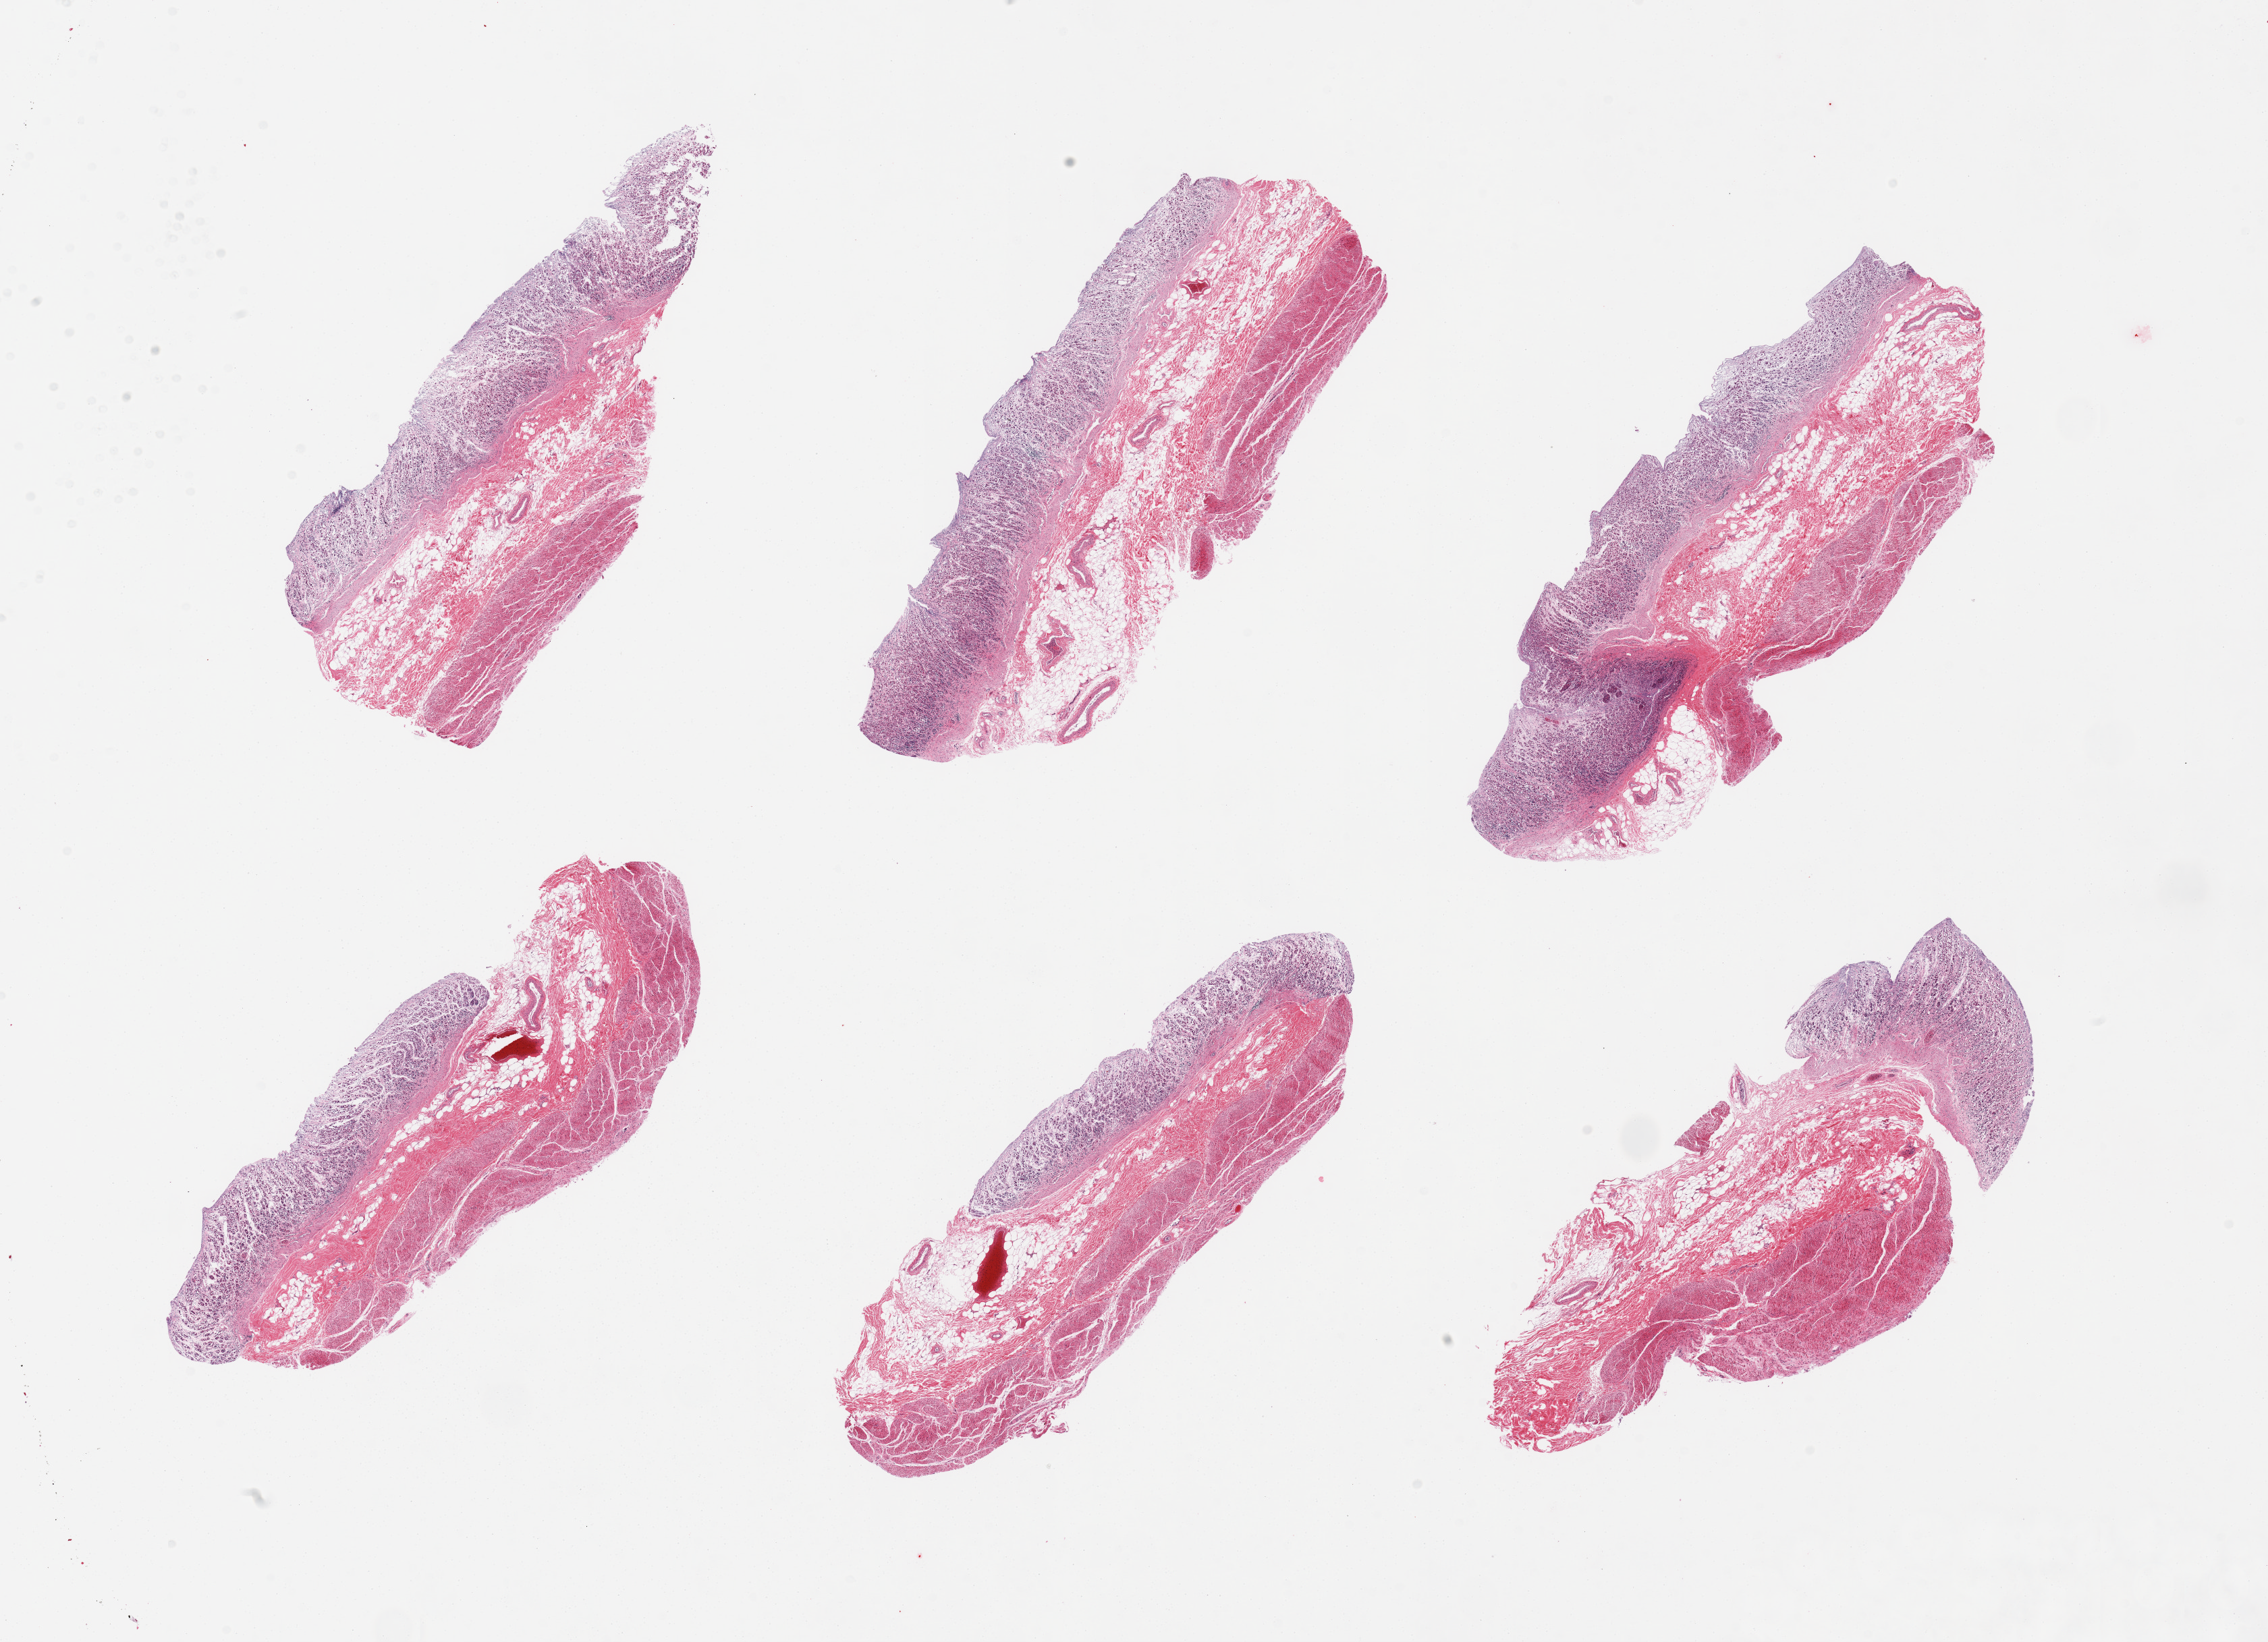
Digitized haematoxylin and eosin-stained section — a low-resolution overview of the entire scanned area, about 26.6 x 19.2 mm; PAXgene-fixed, paraffin-embedded tissue; section of stomach (target tissue); tissue donor sample.
Reviewer comment on this tissue sample: 6pieces; mucosa completely autolyzed; muscle moderately autolyzed.